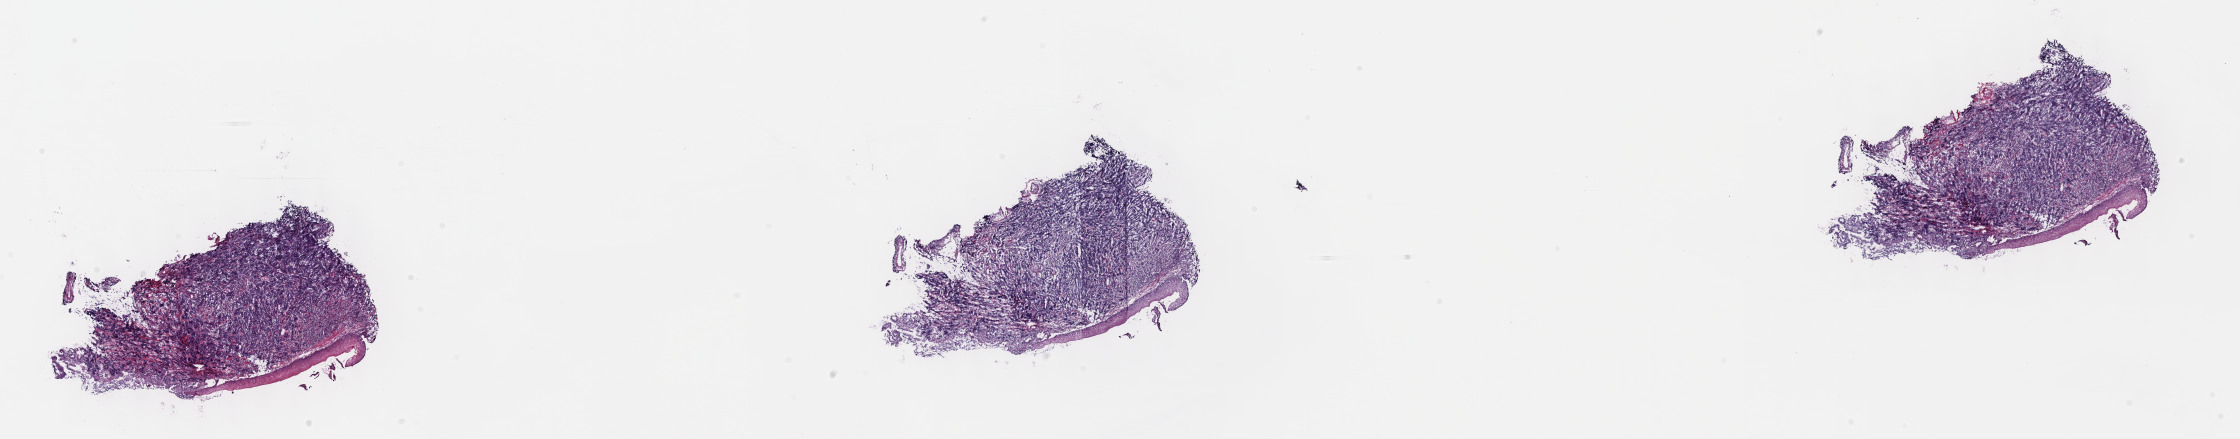
Digitized Hematoxylin and eosin (H&E) stained tissue section (whole slide), a low-resolution overview of the entire scanned area, about 36.2 x 7.1 mm (from a 40x scan), frozen section from the top of the tissue portion, sample: primary tumour, esophagus. Patient: female, age at initial diagnosis 71 years. Histologic grade: GX (grade cannot be assessed). Slide review estimates, as recorded: tumour cells 80%, tumour nuclei 90%, normal cells 10%, stromal cells 10%, necrosis 0%. Infiltration values recorded for this section: lymphocyte infiltration 0%, monocyte infiltration 0%, neutrophil infiltration 0%.
Lymph nodes positive (case pathology): 0 of 10 examined. Pathologic diagnosis: Adenocarcinoma, NOS (lower third of esophagus). AJCC pathologic stage: I.